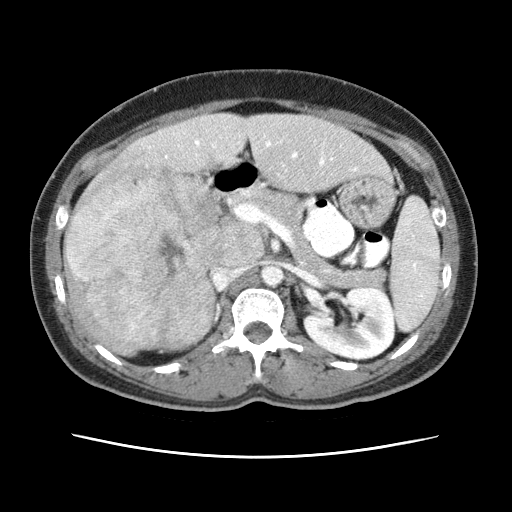
Contrast-enhanced abdominal CT (liver protocol), one axial slice. Position 25 of 79 along the scan axis. 120 kVp. Soft-tissue window (W 400 / L 40 HU). 2.5 mm slice thickness. 512 × 512 image matrix, field of view 340 × 340 mm. Case-level facts recorded for this patient, not image findings: diagnosis: hepatocellular carcinoma (patient treated with transarterial chemoembolisation; whether this scan precedes or follows treatment is not stated here); TNM stage (as recorded): Stage-I; Child-Pugh class: A; tumour differentiation: moderately differentiated; tumour nodularity: uninodular.
Annotated regions visible in this slice (semi-automatically segmented with operator editing):
- abdominal aorta: bounding box <262,267,282,284> (left, top, right, bottom; pixels)
- liver parenchyma outside the tumour (the mass and vessels are separate outlines, so this box may not span the whole liver): <64,113,390,354>
- mass: <65,163,220,355>
- liver vessels: <149,140,356,171>